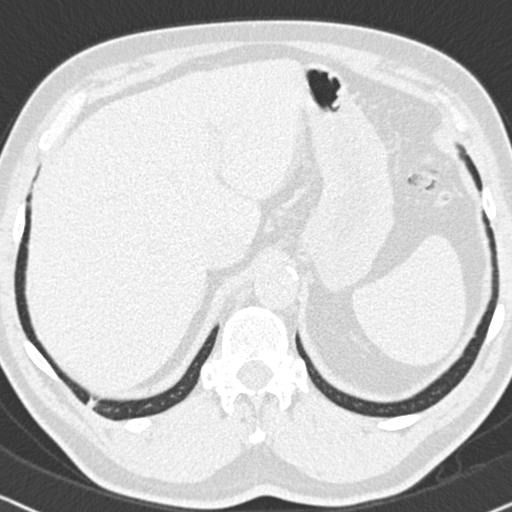
Axial slice from a low-dose chest CT screening exam, first (baseline) screen, lung window (W 1500 / L -600 HU), 2 mm slice thickness, slice 151 of 186 in the series, 512 × 512 image matrix, field of view 325 × 325 mm. Male, age 63 years at enrolment.
Expert reader's lesion annotation, bounding box <75,390,104,417> (left, top, right, bottom; pixels). Screening reader's record for this exam: no non-calcified nodule ≥4 mm recorded. Official screen result: negative screen, no significant abnormalities. Later outcome: lung cancer diagnosed 626 days after this screen (after the second annual screen) — adenocarcinoma, NOS, right lower lobe, moderately differentiated (G2), stage IIIB (AJCC 6th edition), 17 mm at pathology.